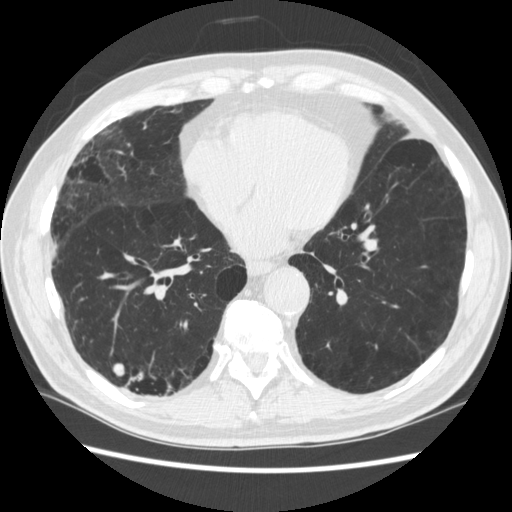
Chest CT (low-dose screening protocol), one axial image; third annual screen; lung window (W 1500 / L -600 HU); 1.25 mm slice thickness; standard (soft-tissue) reconstruction kernel (STANDARD); 120 kVp; 512 × 512 image matrix. Male participant, aged 70 years at enrolment. Former smoker at enrolment.
• Expert reader's lesion annotation, bounding box <130,359,177,413> (left, top, right, bottom; pixels).
• The screening reader recorded 4 non-calcified nodules or masses ≥4 mm on this exam; which of them this box marks is not recorded.
• Official screen result: positive, other.
• Participant outcome: lung cancer diagnosed 253 days after this screen — squamous cell carcinoma, NOS, right upper lobe, poorly differentiated (G3), stage IV (AJCC 6th edition).